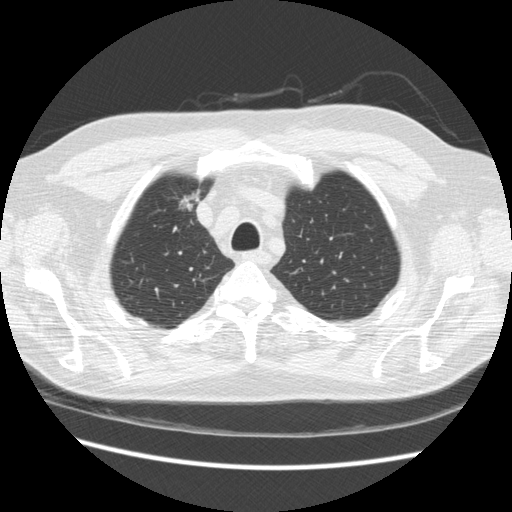
Axial slice from a low-dose chest CT screening exam. Third annual screen. Lung window (W 1500 / L -600 HU). Standard (soft-tissue) reconstruction kernel (STANDARD). Slice 46 of 234 in the series. Male participant, aged 66 years at enrolment. Former smoker at enrolment.
Expert reader's lesion annotation, bounding box <166,181,210,220> (left, top, right, bottom; pixels). No non-calcified nodule or mass ≥4 mm was recorded by the screening reader at this exam. Official screen result: positive, other. Participant outcome: lung cancer diagnosed 229 days after this screen — bronchiolo-alveolar adenocarcinoma, NOS, right upper lobe, moderately differentiated (G2), stage IA (AJCC 6th edition), 12 mm at pathology.